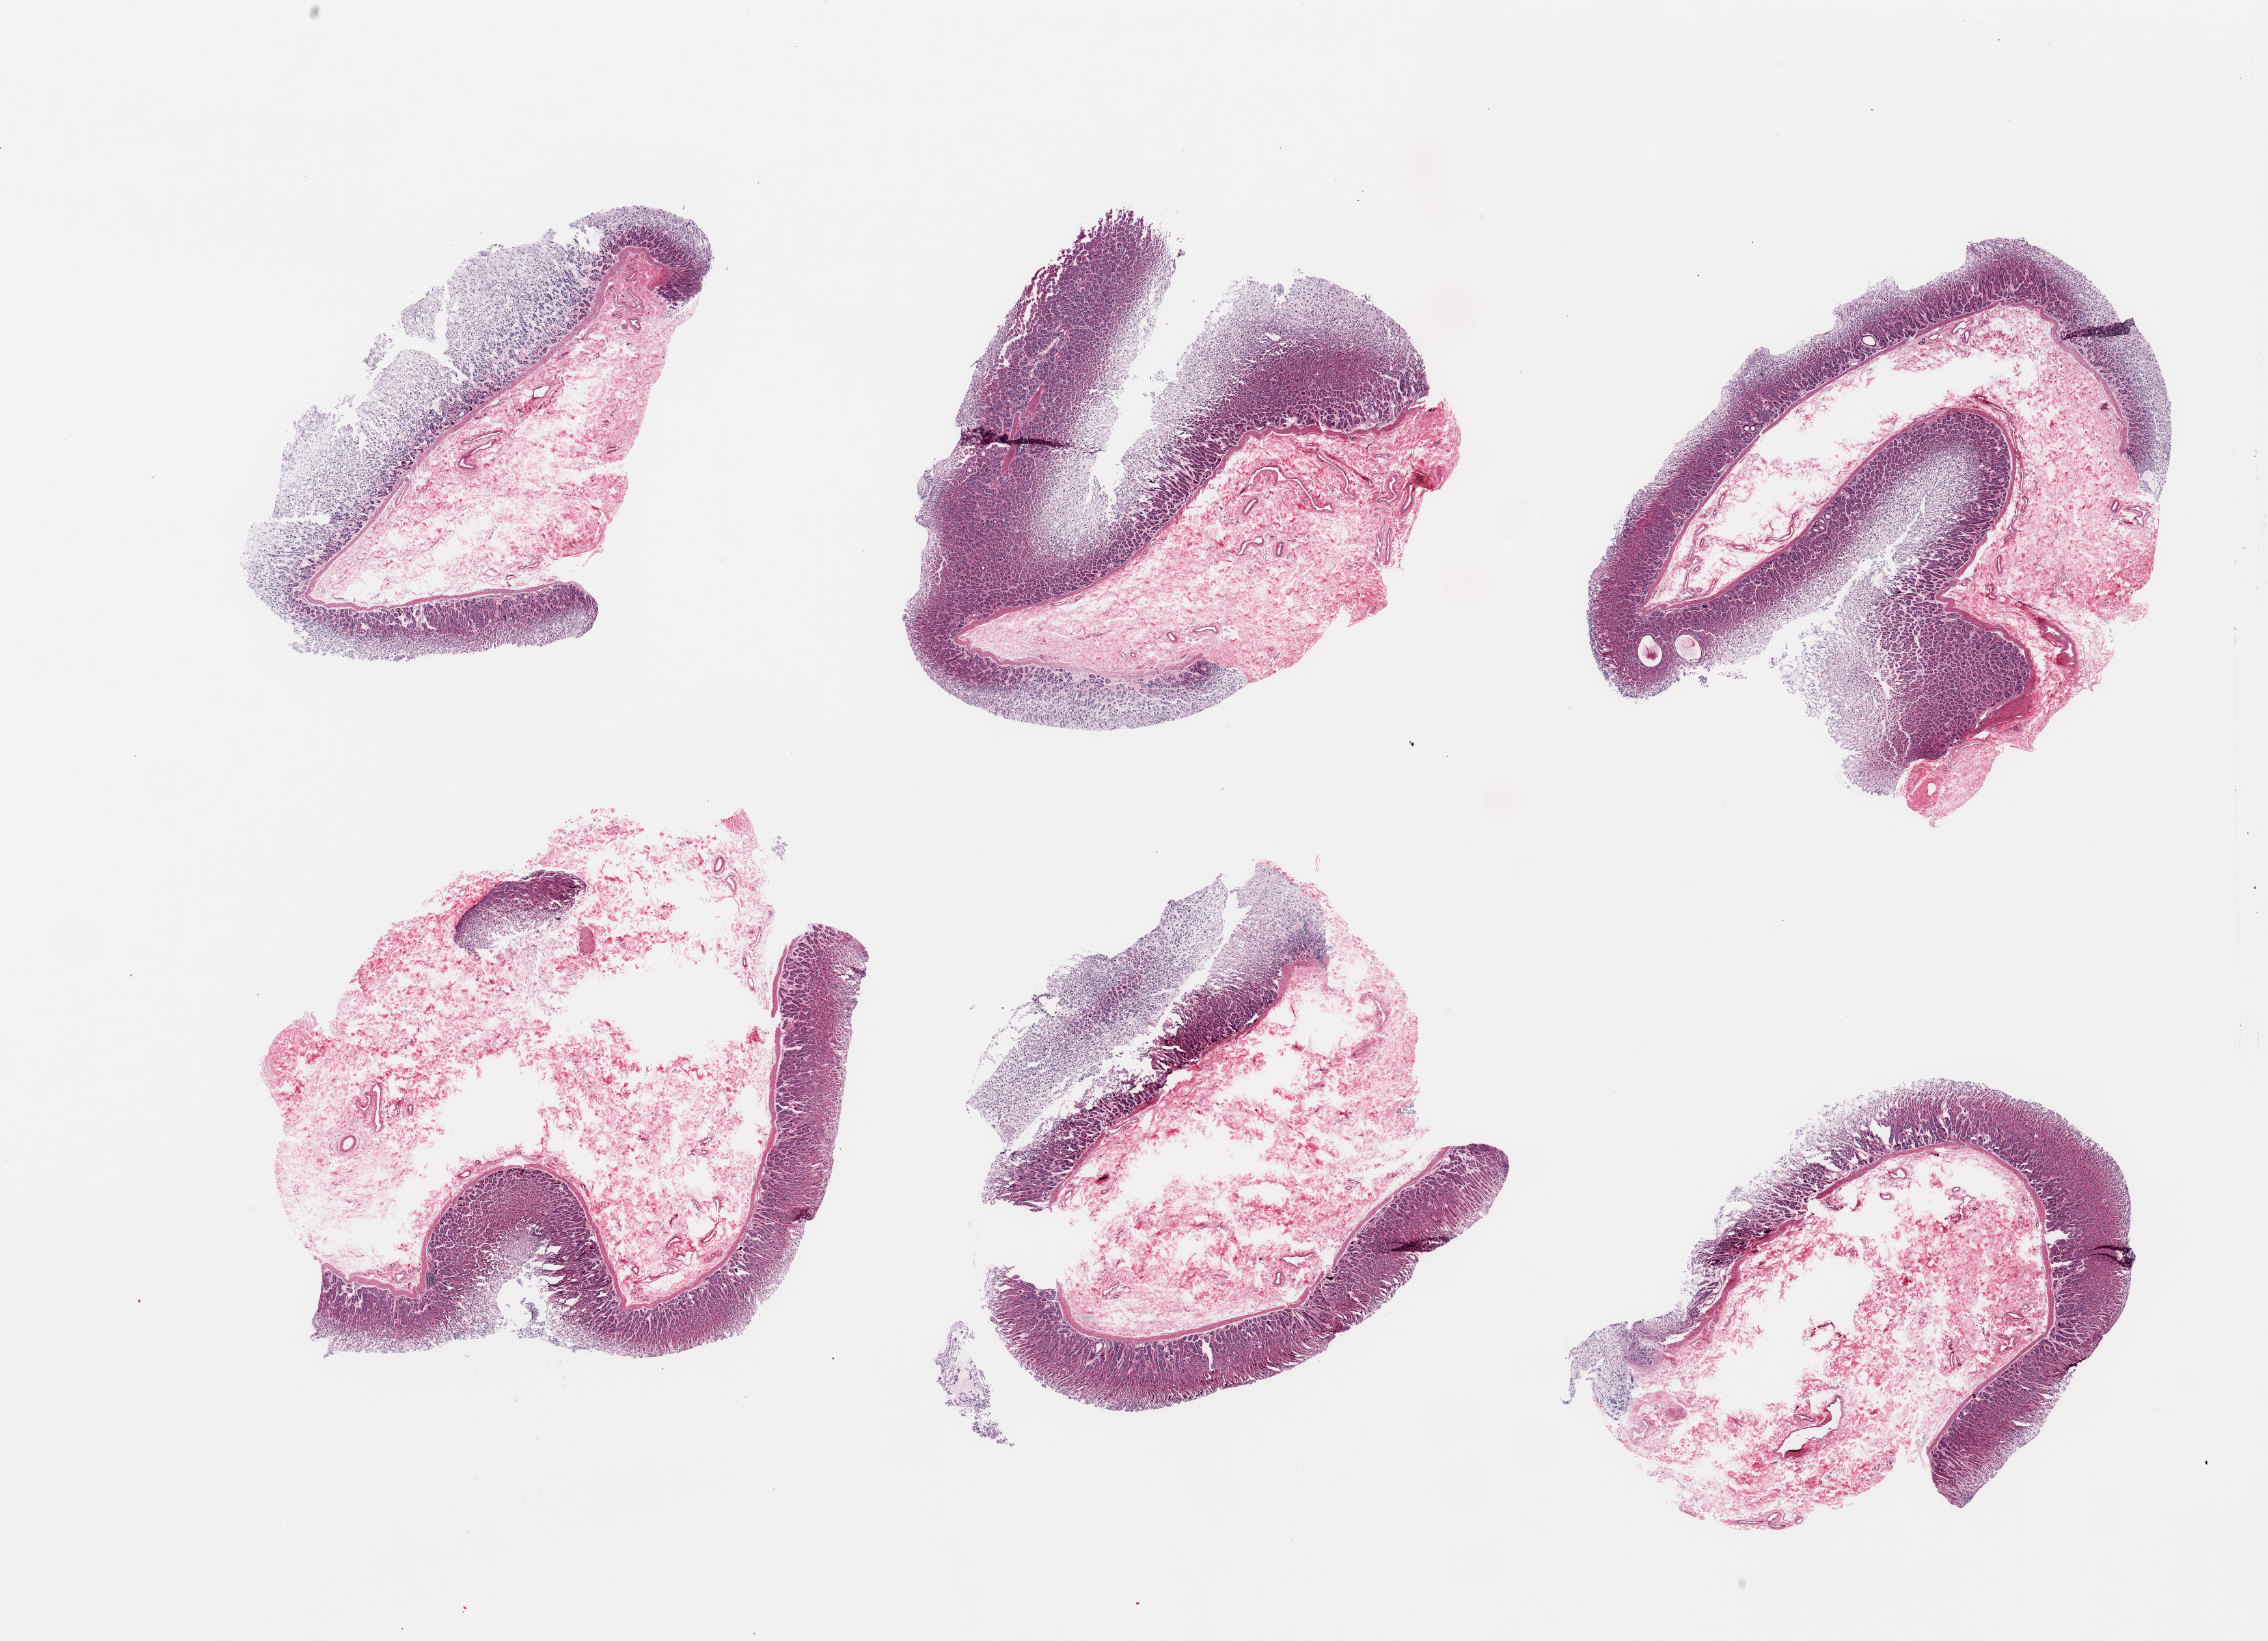
Whole-slide image, H&E stain — shown as a low-resolution overview of the whole scanned area (about 27.6 x 19.9 mm); PAXgene-fixed, paraffin-embedded tissue; sampled site (target tissue): stomach; donor tissue sample. Donor sex: male.
Pathologist's review note for this sample: 6 pieces, target mucosa up to ~1mm, variably preserved.